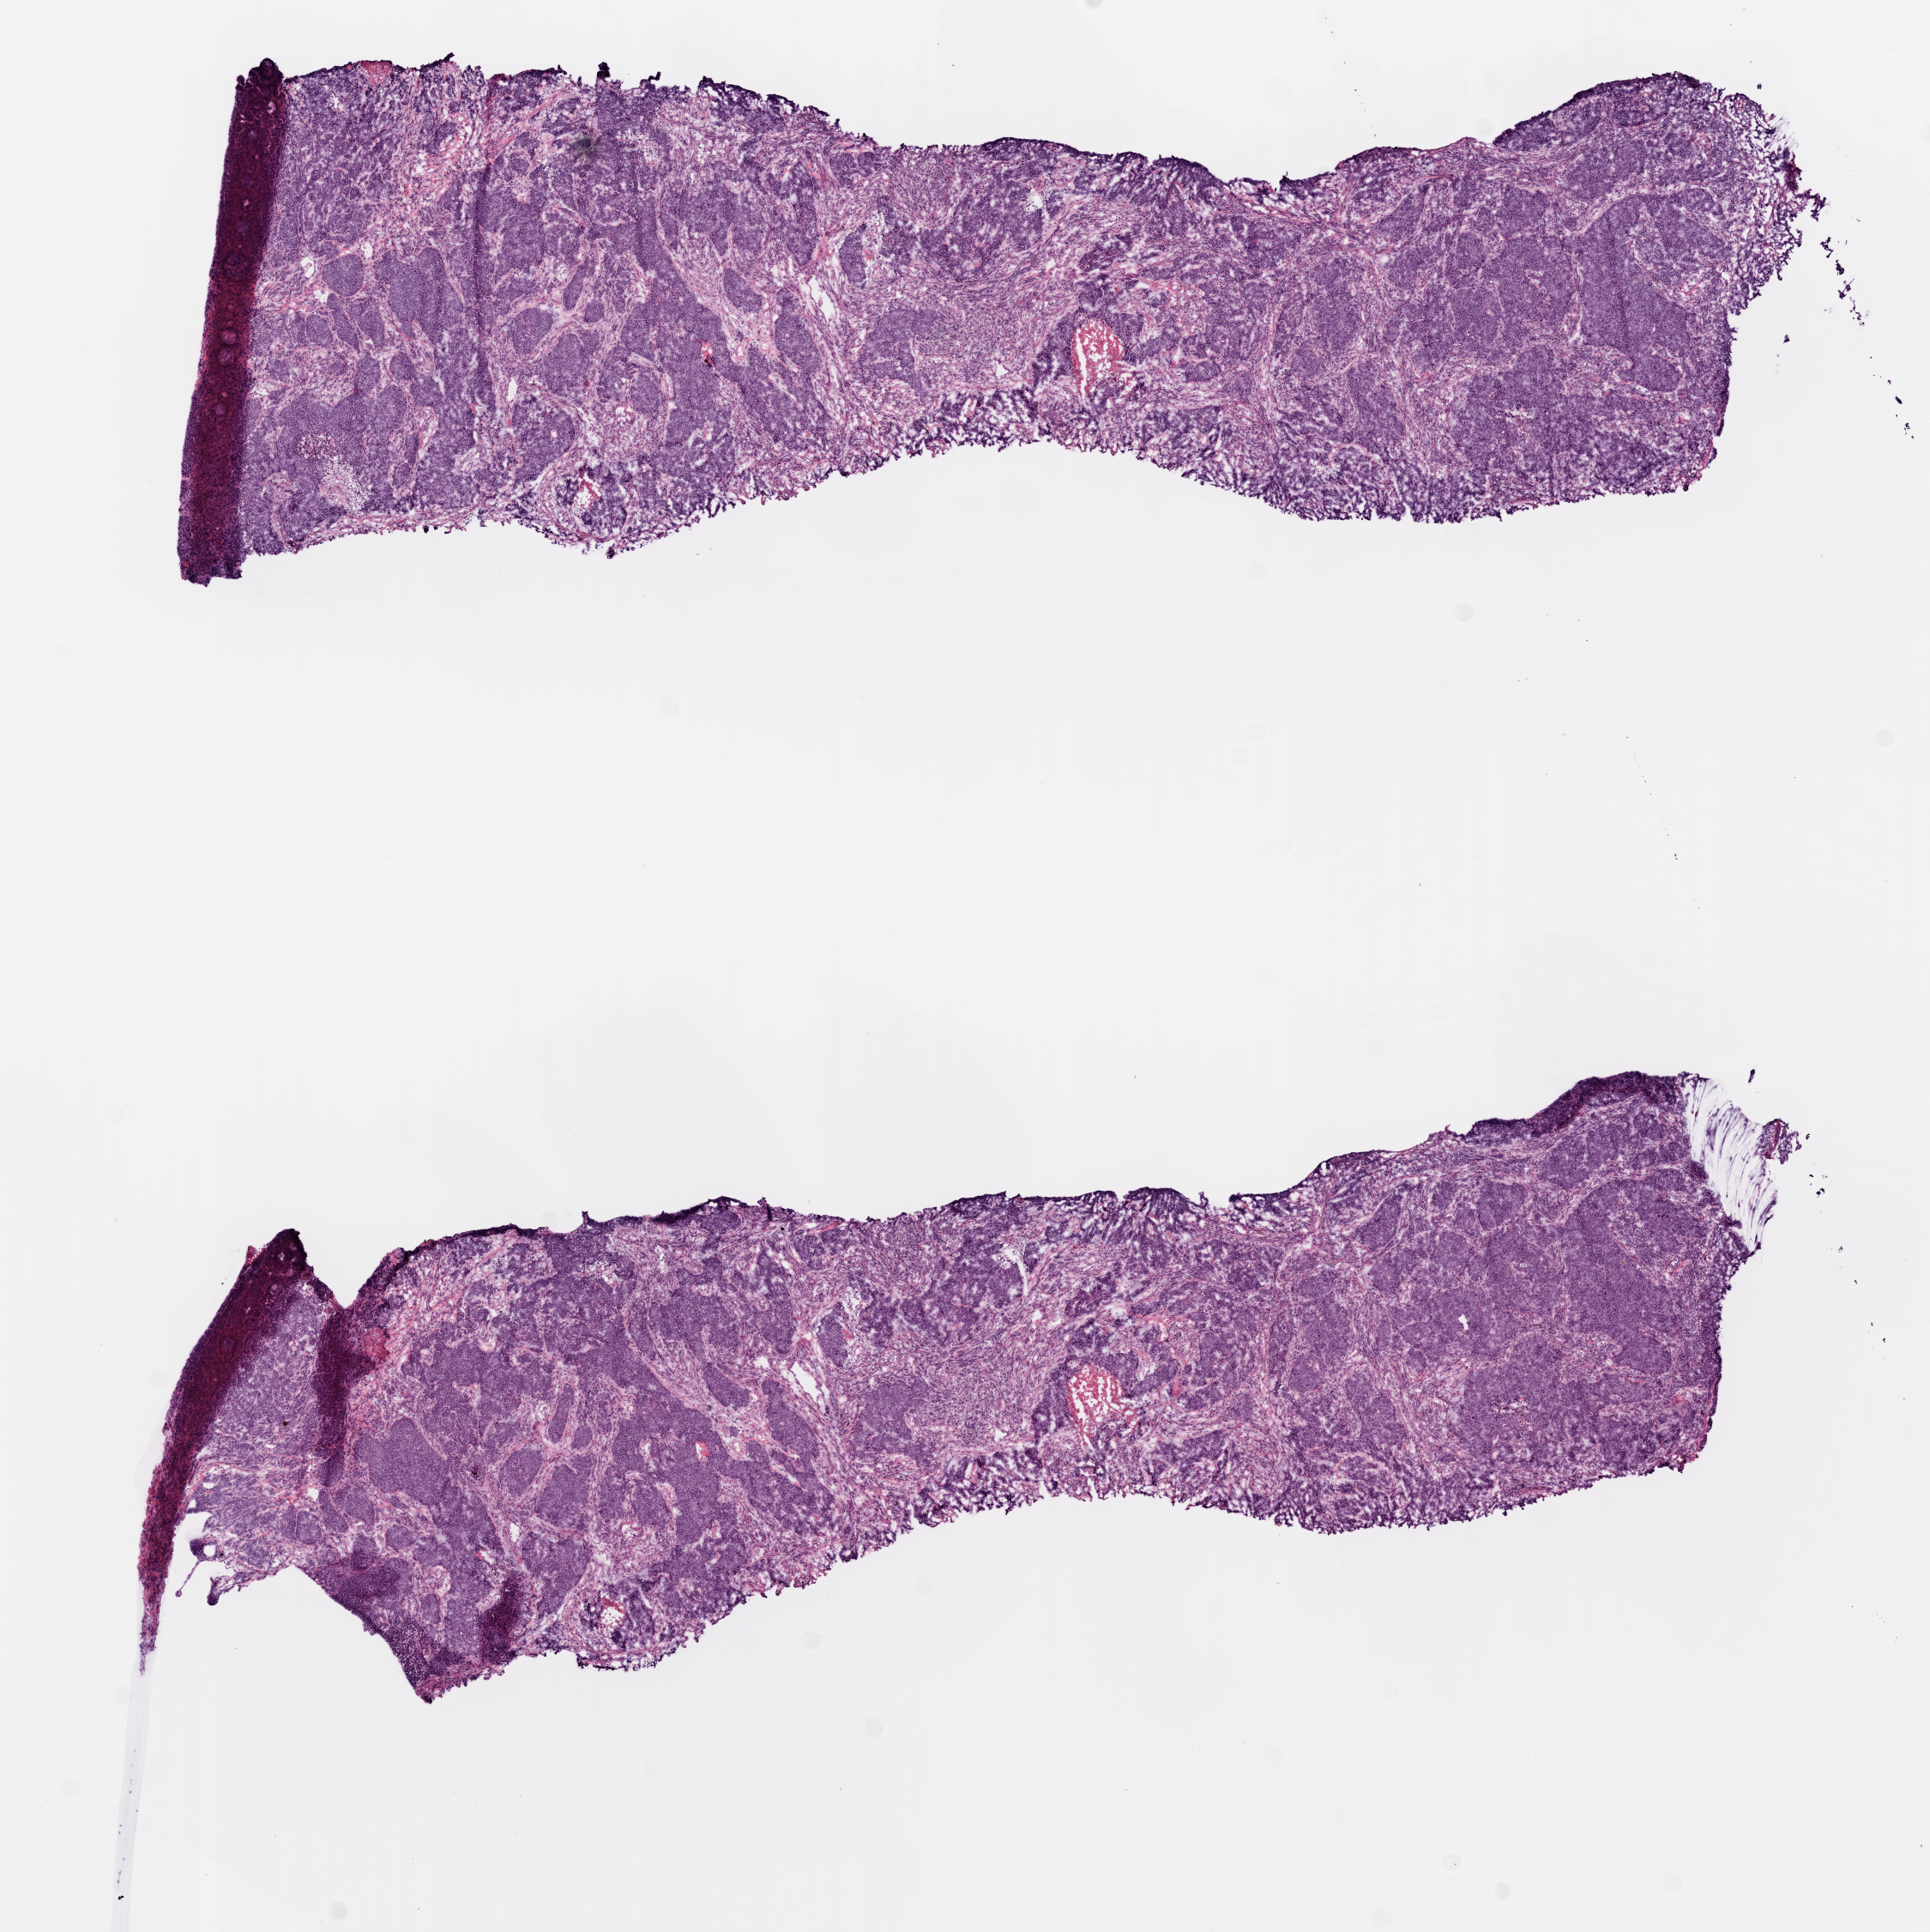
Whole-slide histology image, Hematoxylin and eosin (H&E) stained — whole scanned area (about 9.0 x 9.0 mm, from a 20x scan) shown as a low-resolution overview, frozen section from the top of the tissue portion, primary tumour sample from the lung. Patient: female, age at initial diagnosis 65 years. Slide review estimates, as recorded: tumour cells 80%, tumour nuclei 80%, normal cells 0%, stromal cells 15%, necrosis 5%.
* histologic diagnosis: Squamous cell carcinoma, NOS (upper lobe, lung)
* AJCC pathologic stage: IA (6th edition)